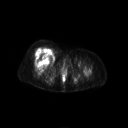
FDG PET of an extremity soft-tissue mass (from a PET/CT study), one axial slice. Slice 56 of 267 in the series (ordered by position). 3.27 mm slice thickness. 128 × 128 image matrix, field of view 700 × 700 mm. Female patient, age 56 years. Case-level facts recorded for this patient, not image findings: histological type: malignant solitary fibrous tumor; grade: intermediate; site of the primary tumour: right thigh.
Outlined on this slice (expert contour drawn on MRI and transferred to this co-registered scan by the dataset authors):
- gross tumour volume including surrounding oedema: bounding box <33,47,53,62> (left, top, right, bottom; pixels)
- gross tumour volume (mass): <33,48,53,62>